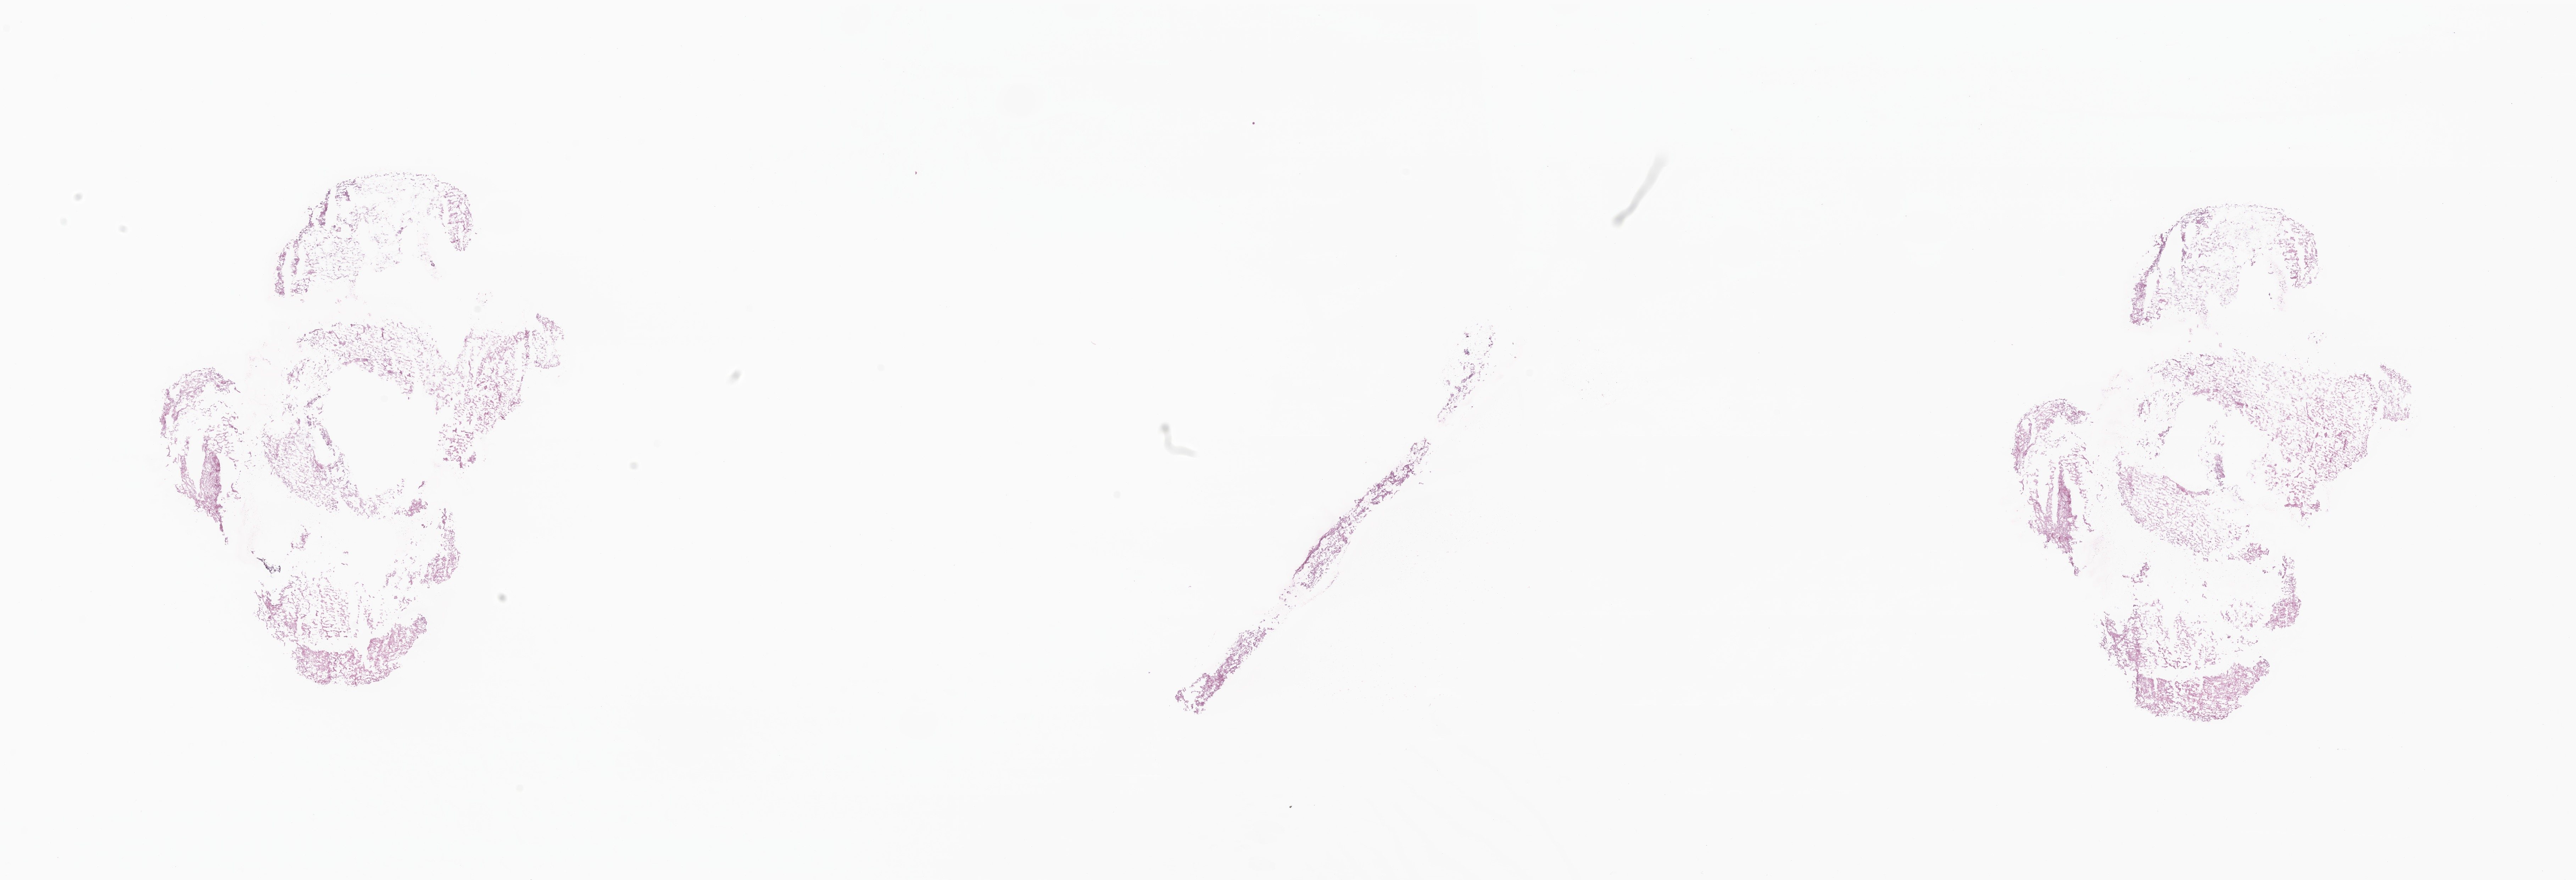
Digitized hematoxylin and eosin (H&E)-stained section of tumor tissue from the brain — shown as a low-resolution overview of the whole scanned area (about 30.6 x 10.5 mm), cryosection (OCT / tissue freezing medium). Patient: male, age 165 months (13 years 9 months).
Diagnosis (ICD-O-3 morphology term): Neoplasm, uncertain whether benign or malignant.